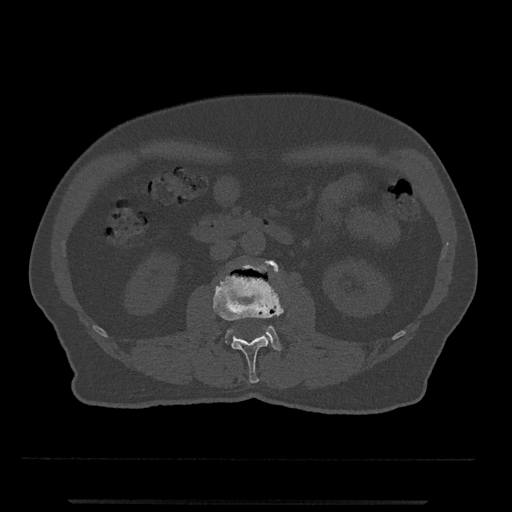
CT including the spine, one axial slice. Position 245 of 797 along the scan axis. Reconstruction kernel Br40s/3. Bone window (W 1800 / L 400 HU). 0.5 mm slice thickness. 512 × 512 image matrix. Male patient, age 63 years. From the clinical record (not read from this slice): primary cancer: prostate.
Outlined on this slice (semi-automatic segmentation, software-assisted and operator-edited):
- L2 vertebra: bounding box [x1, y1, x2, y2] px = [213, 264, 283, 383]
- L3 vertebra: [226, 260, 281, 351]